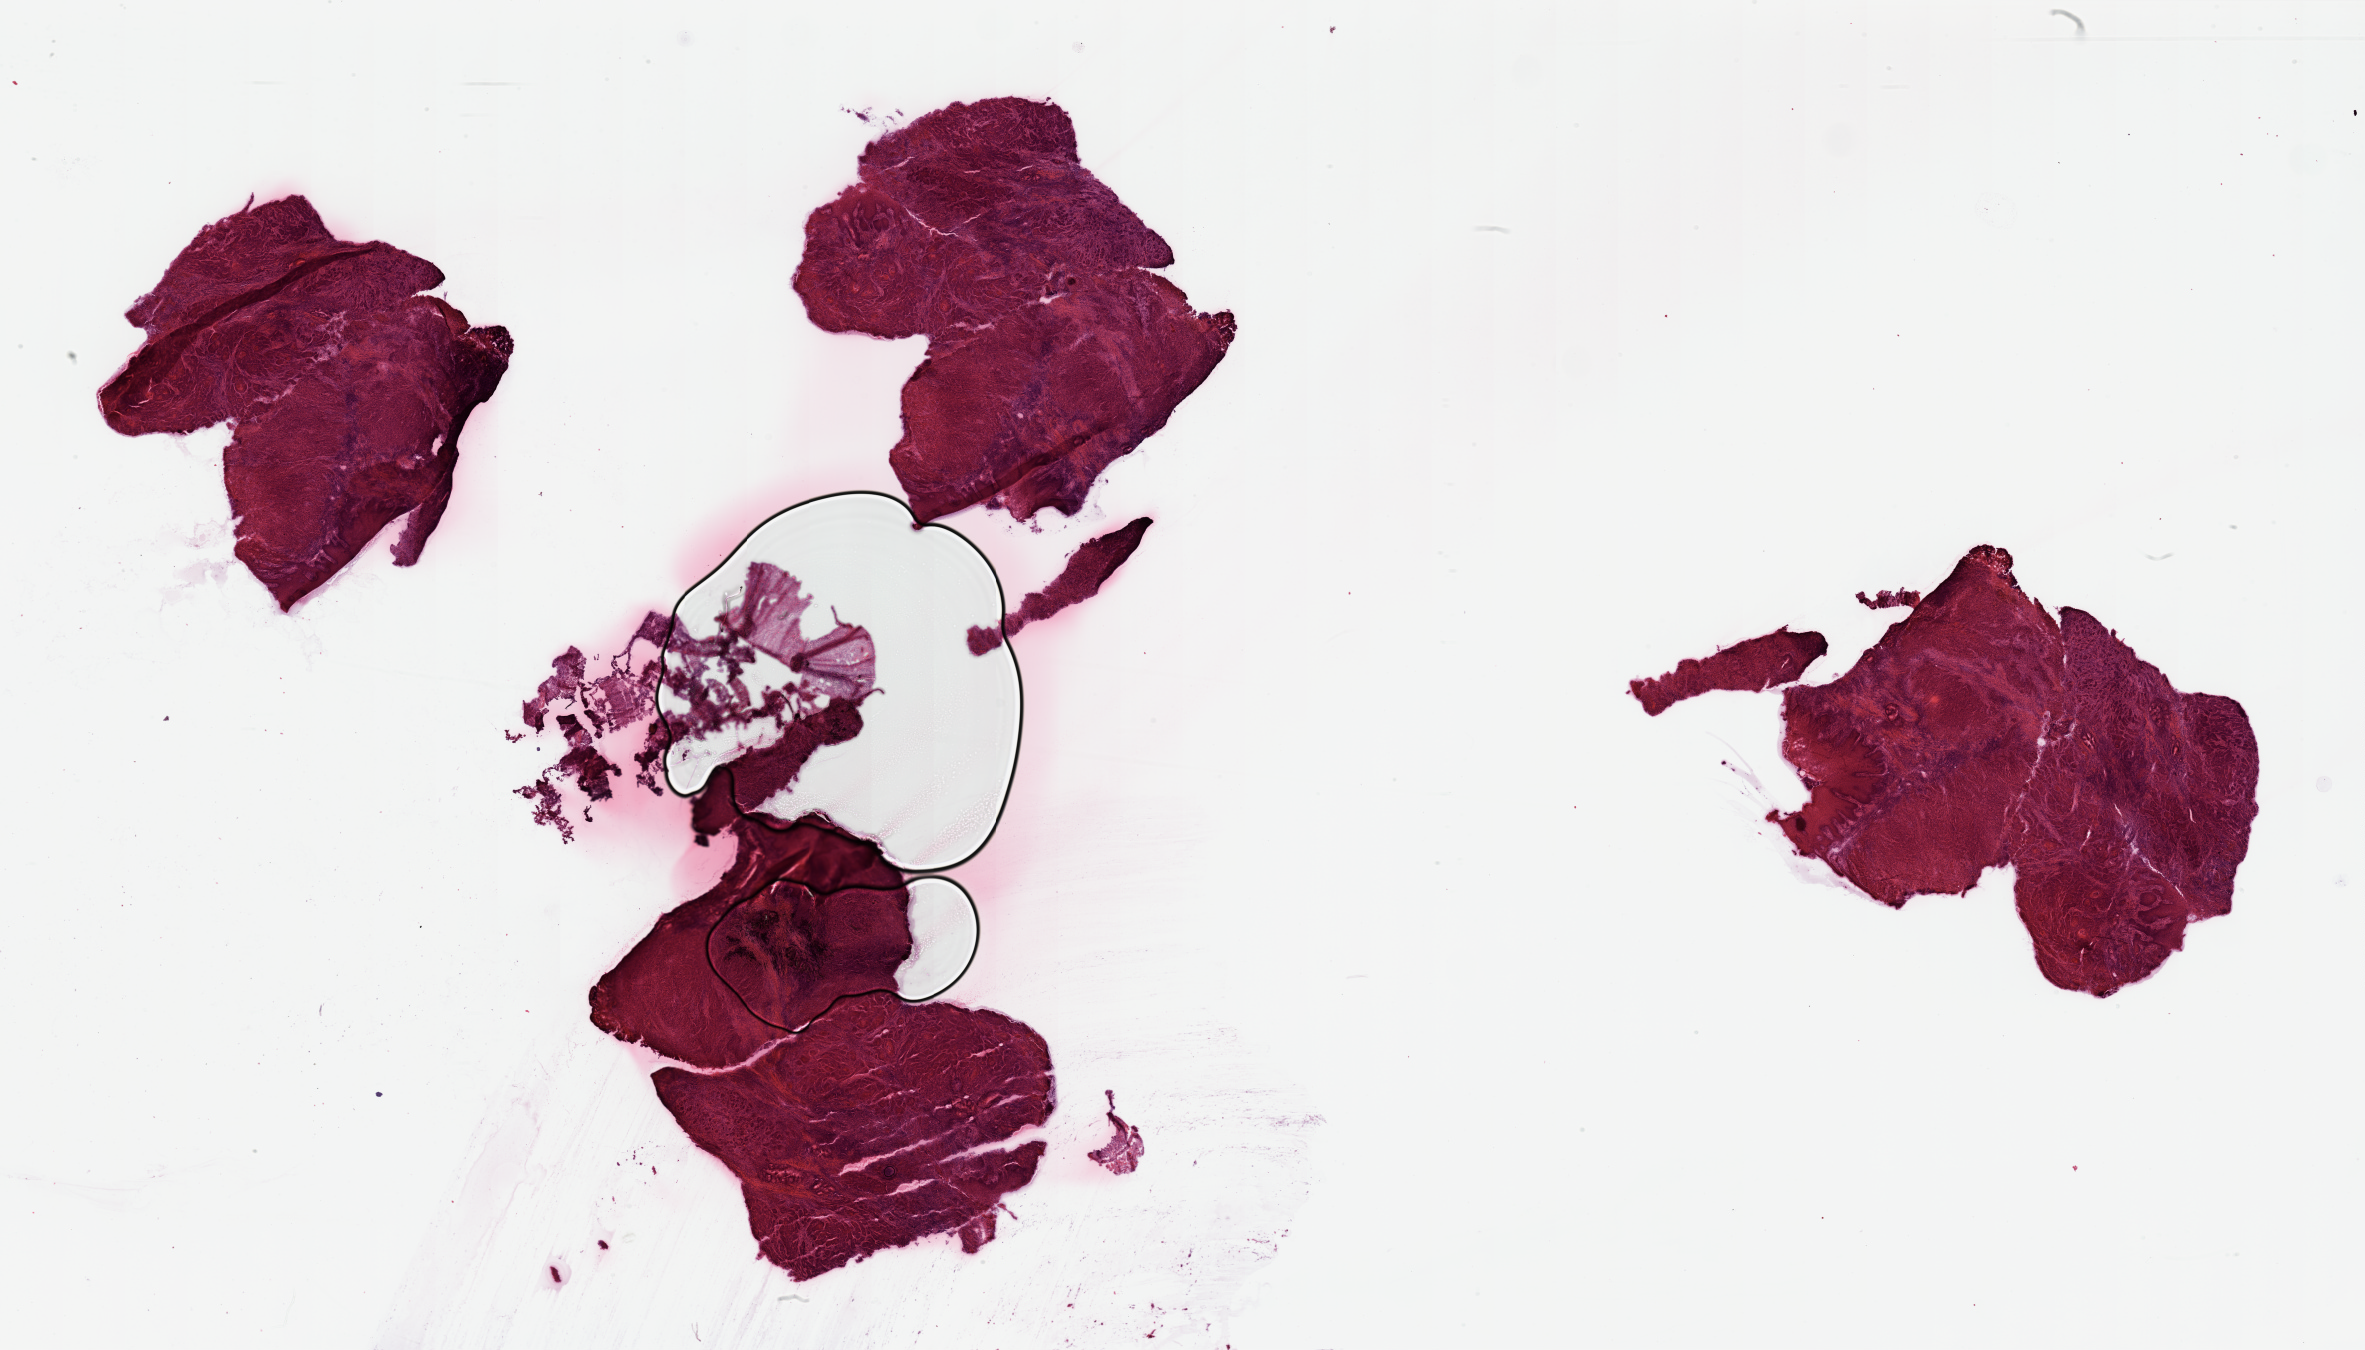
Whole-slide histology image, H&E — shown as a low-resolution overview of the whole scanned area (about 37.4 x 21.4 mm, acquisition: 20x scan). Tumour tissue sample, sampled site: larynx. Patient: male, age 50 years. Slide review estimates, as recorded: tumour nuclei 85%, necrosis 5%.
Diagnosis: Squamous cell carcinoma, NOS (larynx, NOS).